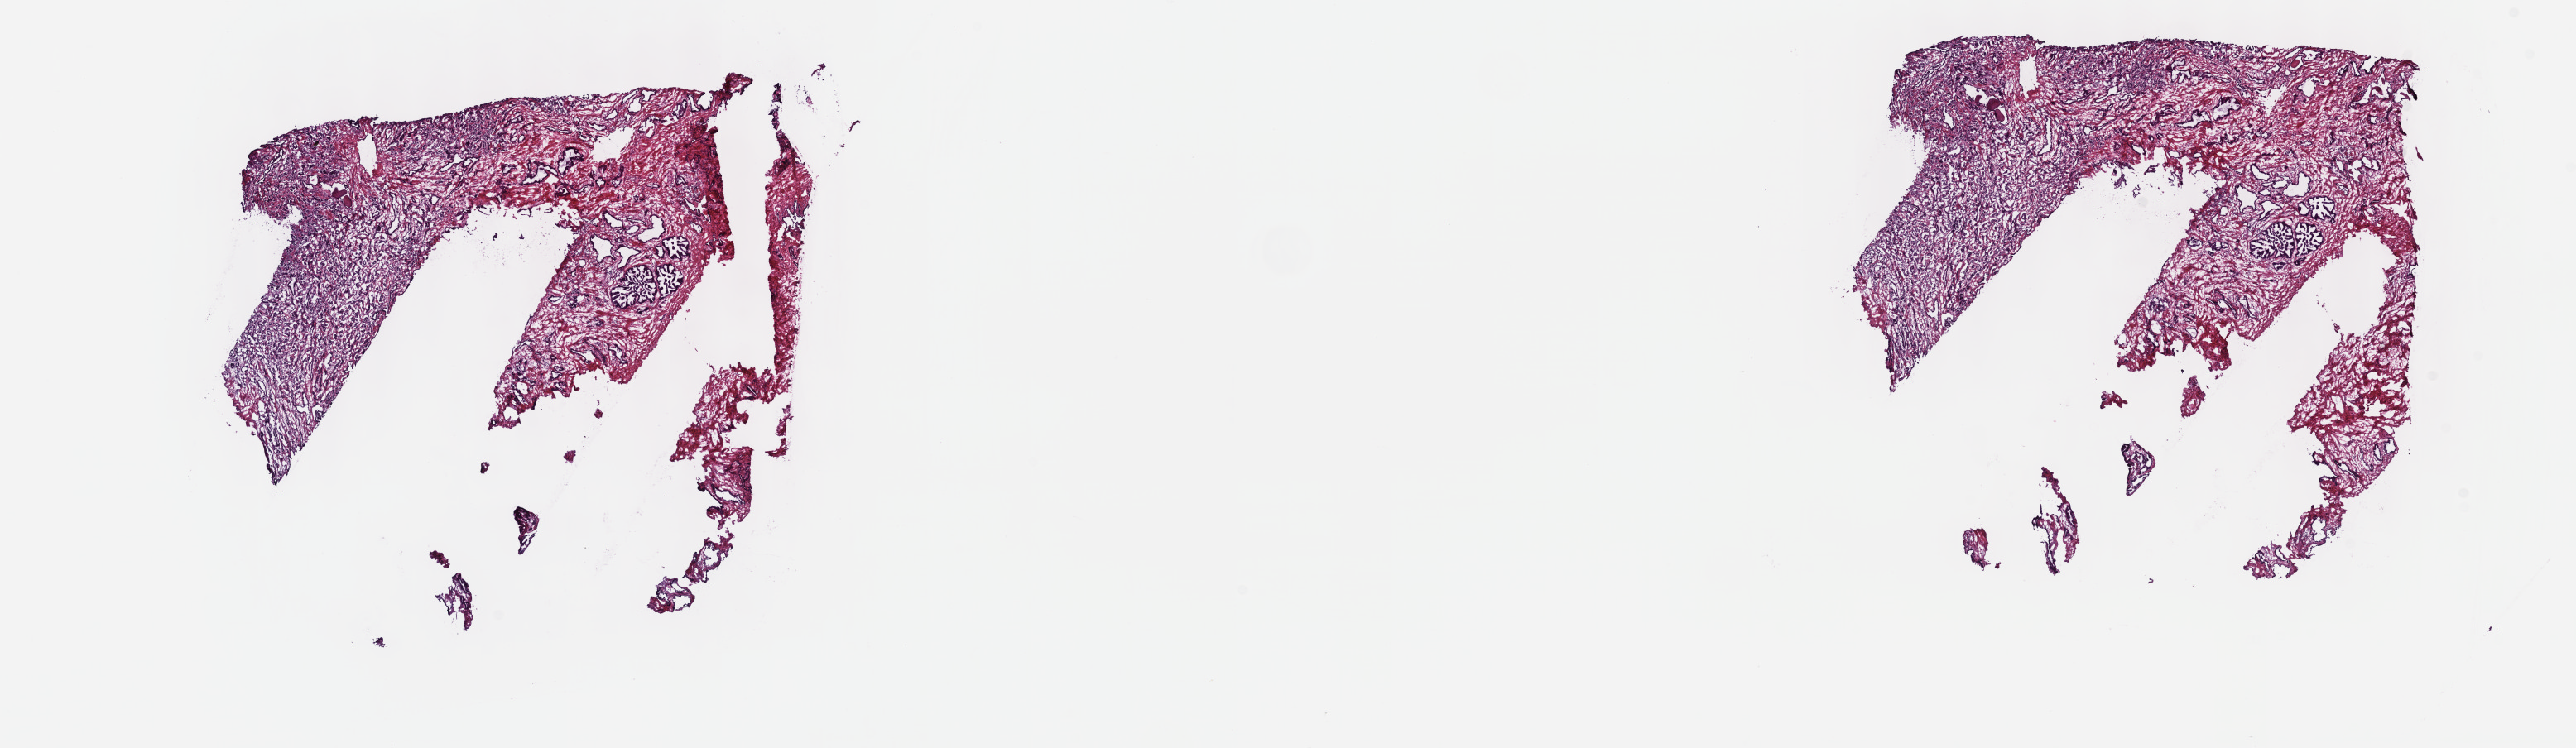
Digitized Hematoxylin and eosin (H&E) stained tissue section (whole slide) — low-resolution overview of the scanned area, about 25.2 x 7.3 mm, frozen section from the top of the tissue portion, primary tumour sample from the prostate. Male patient; age at initial diagnosis 61 years. Gleason score: 7 (3+4). Slide review estimates, as recorded: tumour cells 35%, tumour nuclei 60%, normal cells 15%, stromal cells 50%, necrosis 0%. Inflammatory infiltration, as recorded: lymphocyte infiltration 0%, monocyte infiltration 0%, neutrophil infiltration 0%.
Laterality: bilateral. Pathologic diagnosis: Adenocarcinoma, NOS (prostate gland).